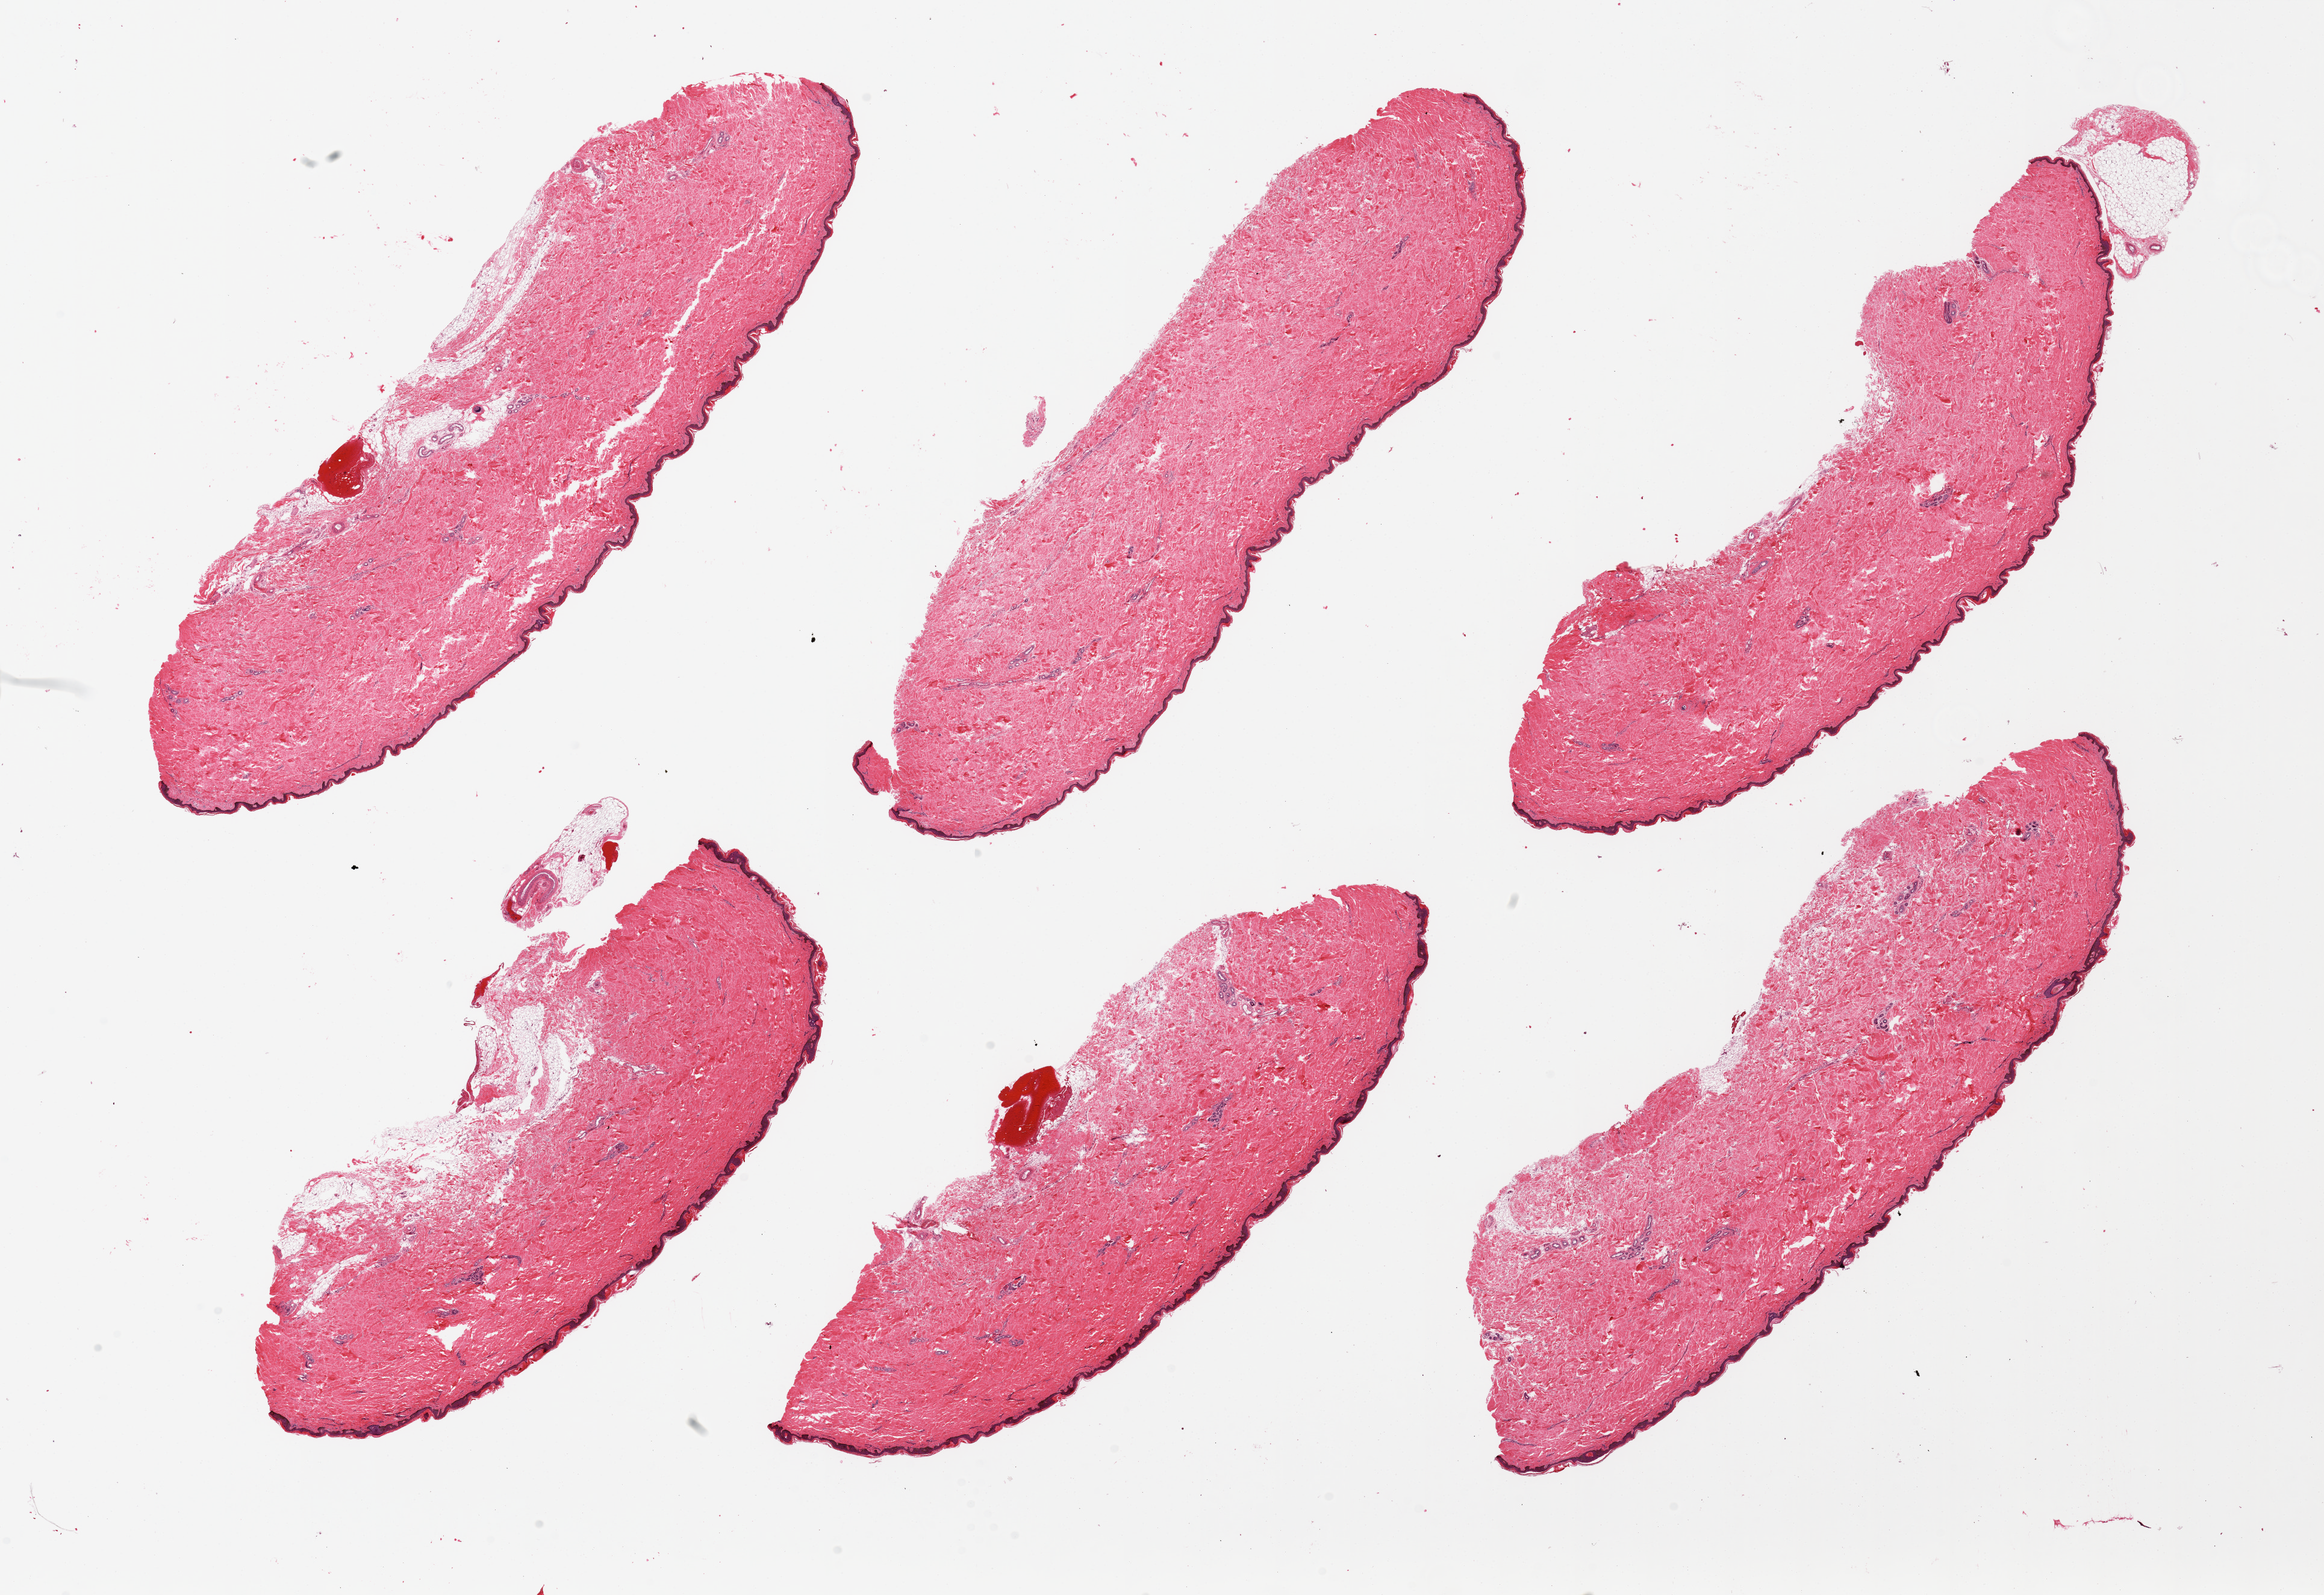
Whole-slide image, H&E stain, a low-resolution overview of the entire scanned area, about 30.5 x 20.9 mm. PAXgene-fixed, paraffin-embedded tissue. Target tissue: skin of suprapubic region. Tissue donor sample. Donor sex: male.
Pathologist's review note for this sample: 6 pieces. Well trimmed.